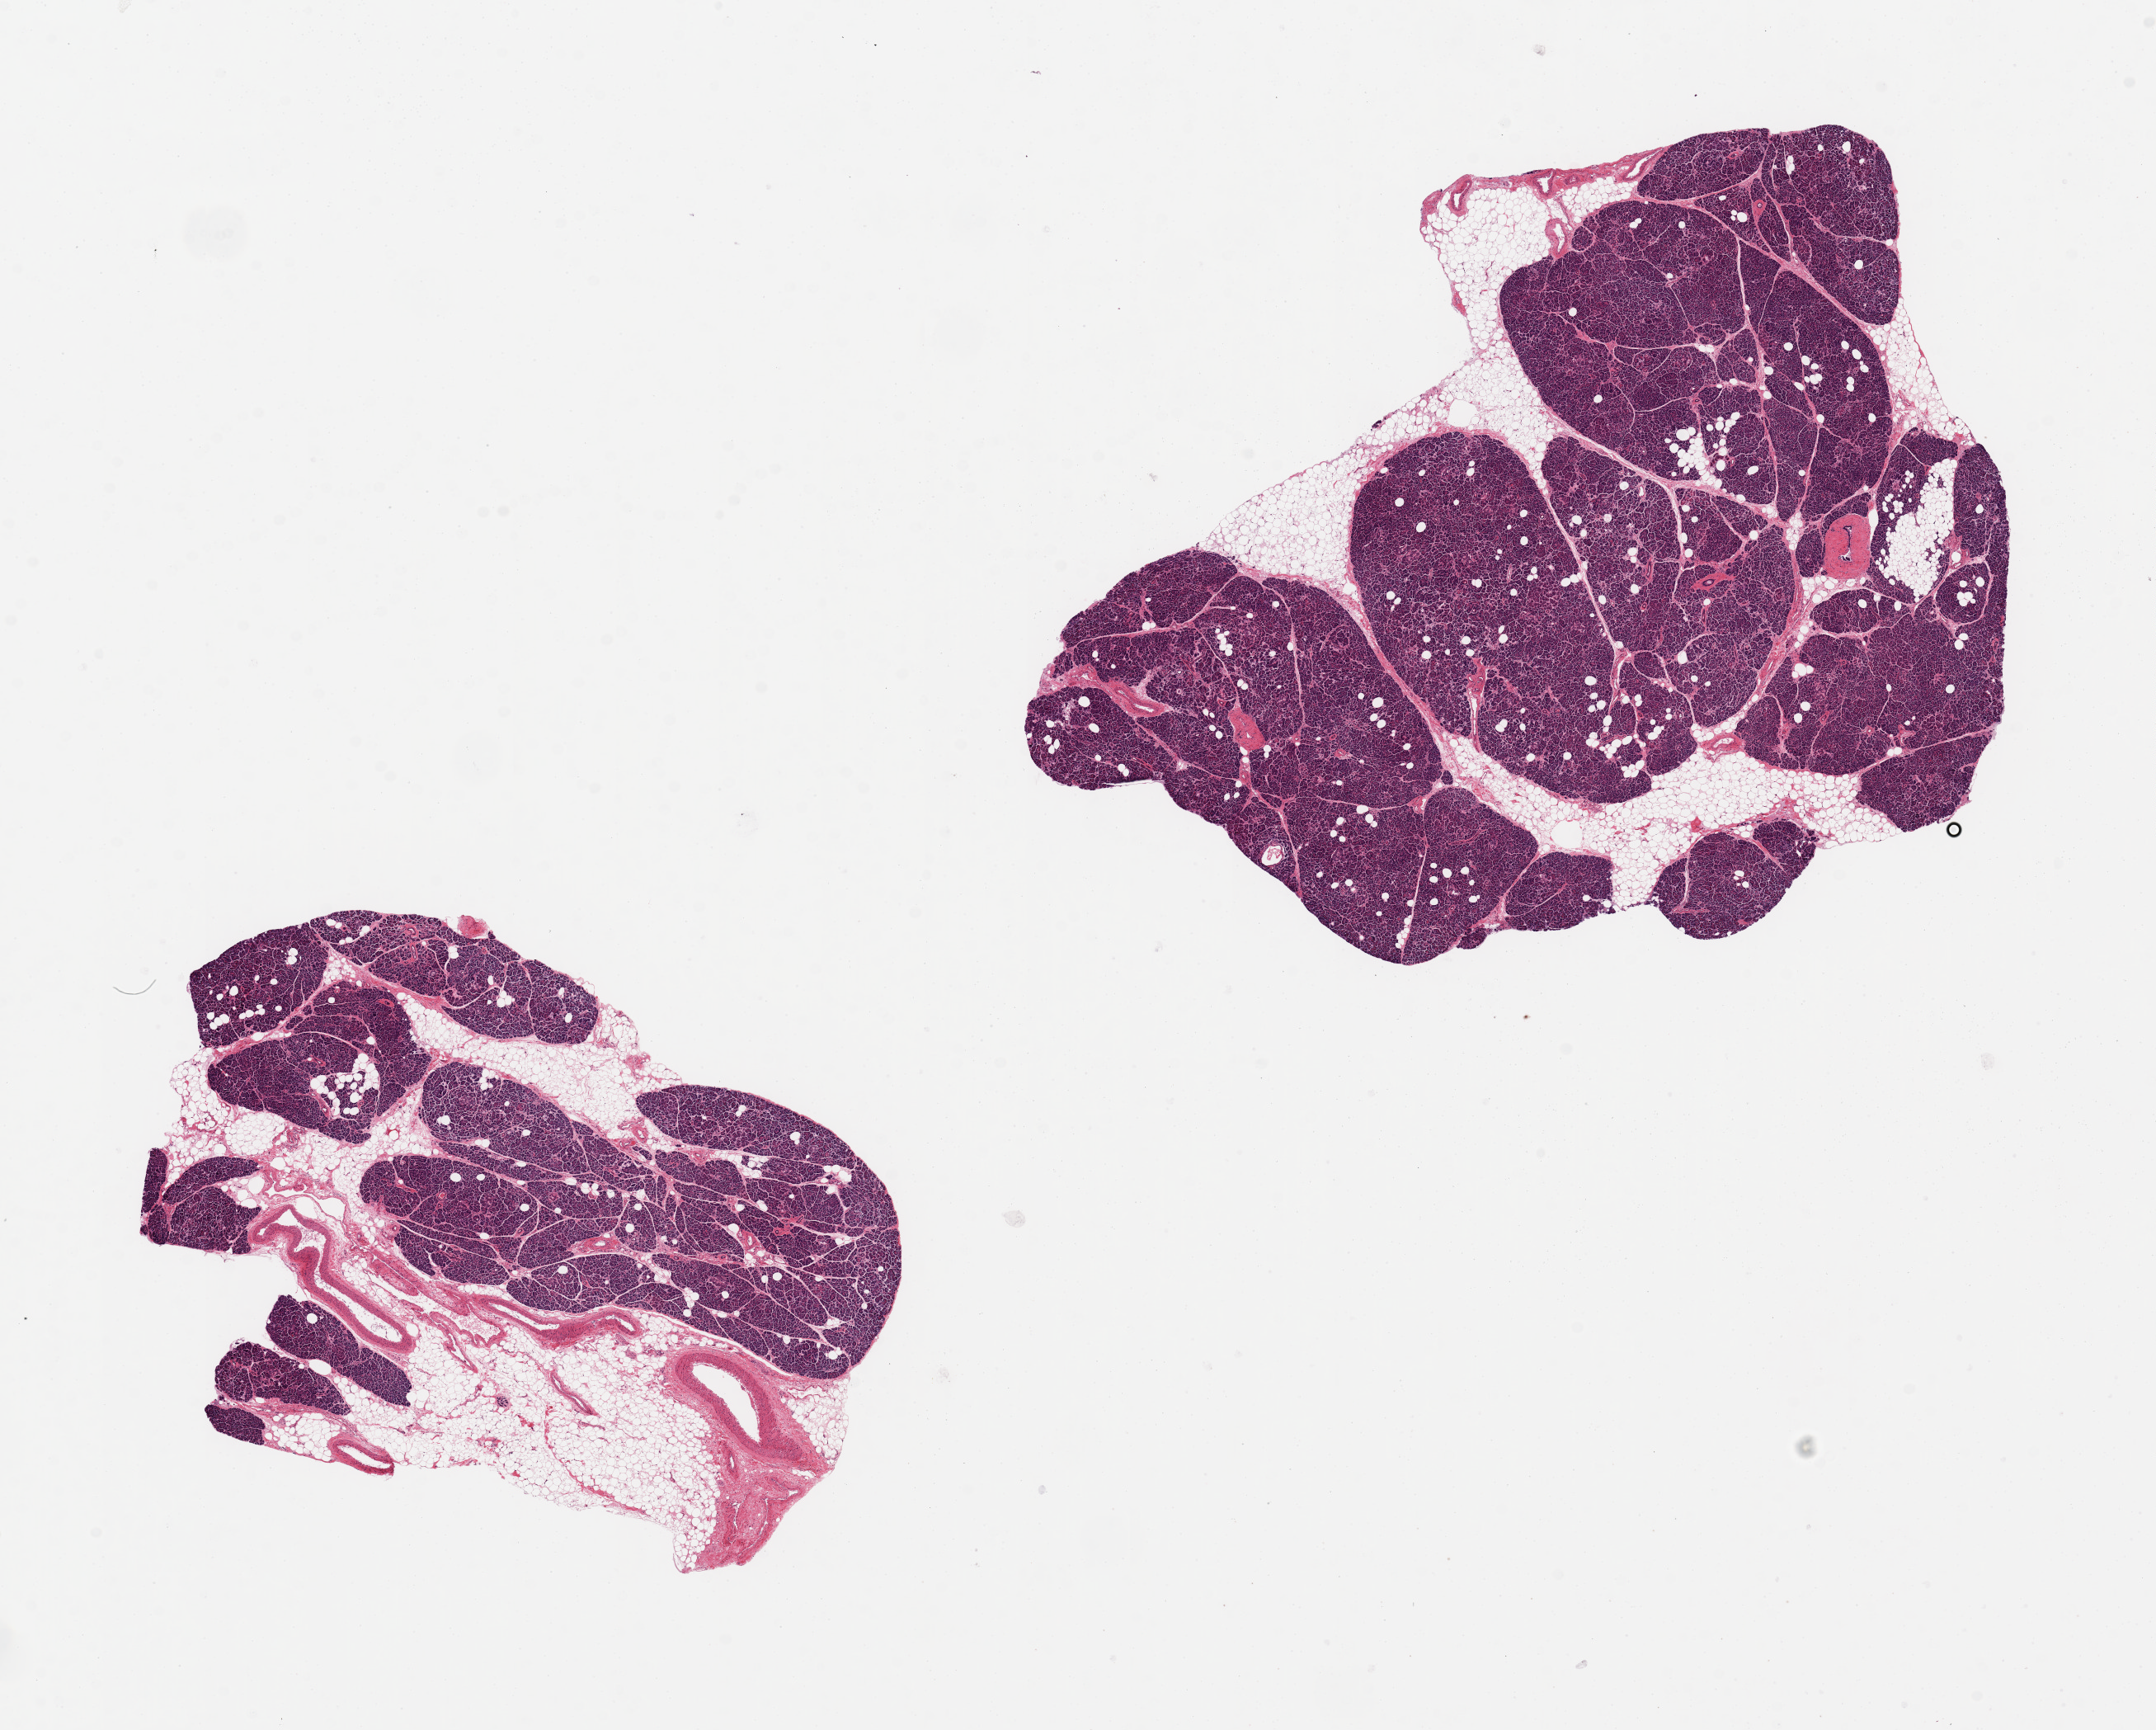
Hematoxylin and eosin (H&E) whole-slide image, brightfield — a low-resolution overview of the entire scanned area, about 20.7 x 16.6 mm (acquisition: 20x scan). PAXgene-fixed paraffin-embedded (PFPE) section. Target tissue: pancreas. Tissue donor sample. Donor: male.
* pathologist's review note for this sample: 2 pieces, 10x8 & 7x5mm;20-50% adipose intermixed with parenchyma; few islets